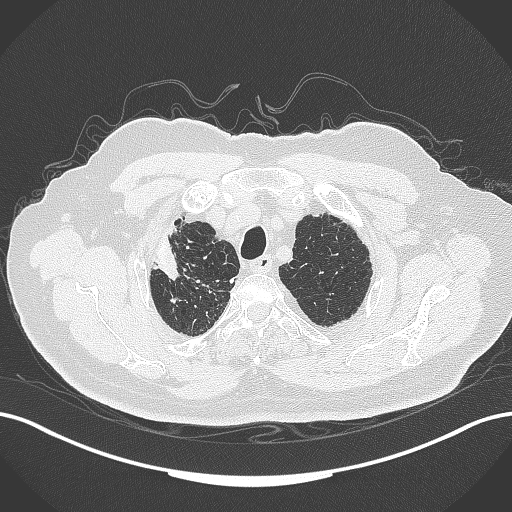
Chest CT, one axial slice. Position 309 of 389 along the scan axis. Reconstruction kernel B70f. 120 kVp. Lung window (W 1500 / L -600 HU). 1 mm slice thickness. 512 × 512 image matrix, field of view 400 × 400 mm. Male patient, age 72 years. Case-level facts recorded for this patient, not image findings: clinical TNM (as recorded): T1a N0 M0.
Annotated regions visible in this slice (bounding box drawn by a radiologist):
- lung tumour (recorded histology: squamous cell carcinoma): bounding box <150,229,181,286> (left, top, right, bottom; pixels)